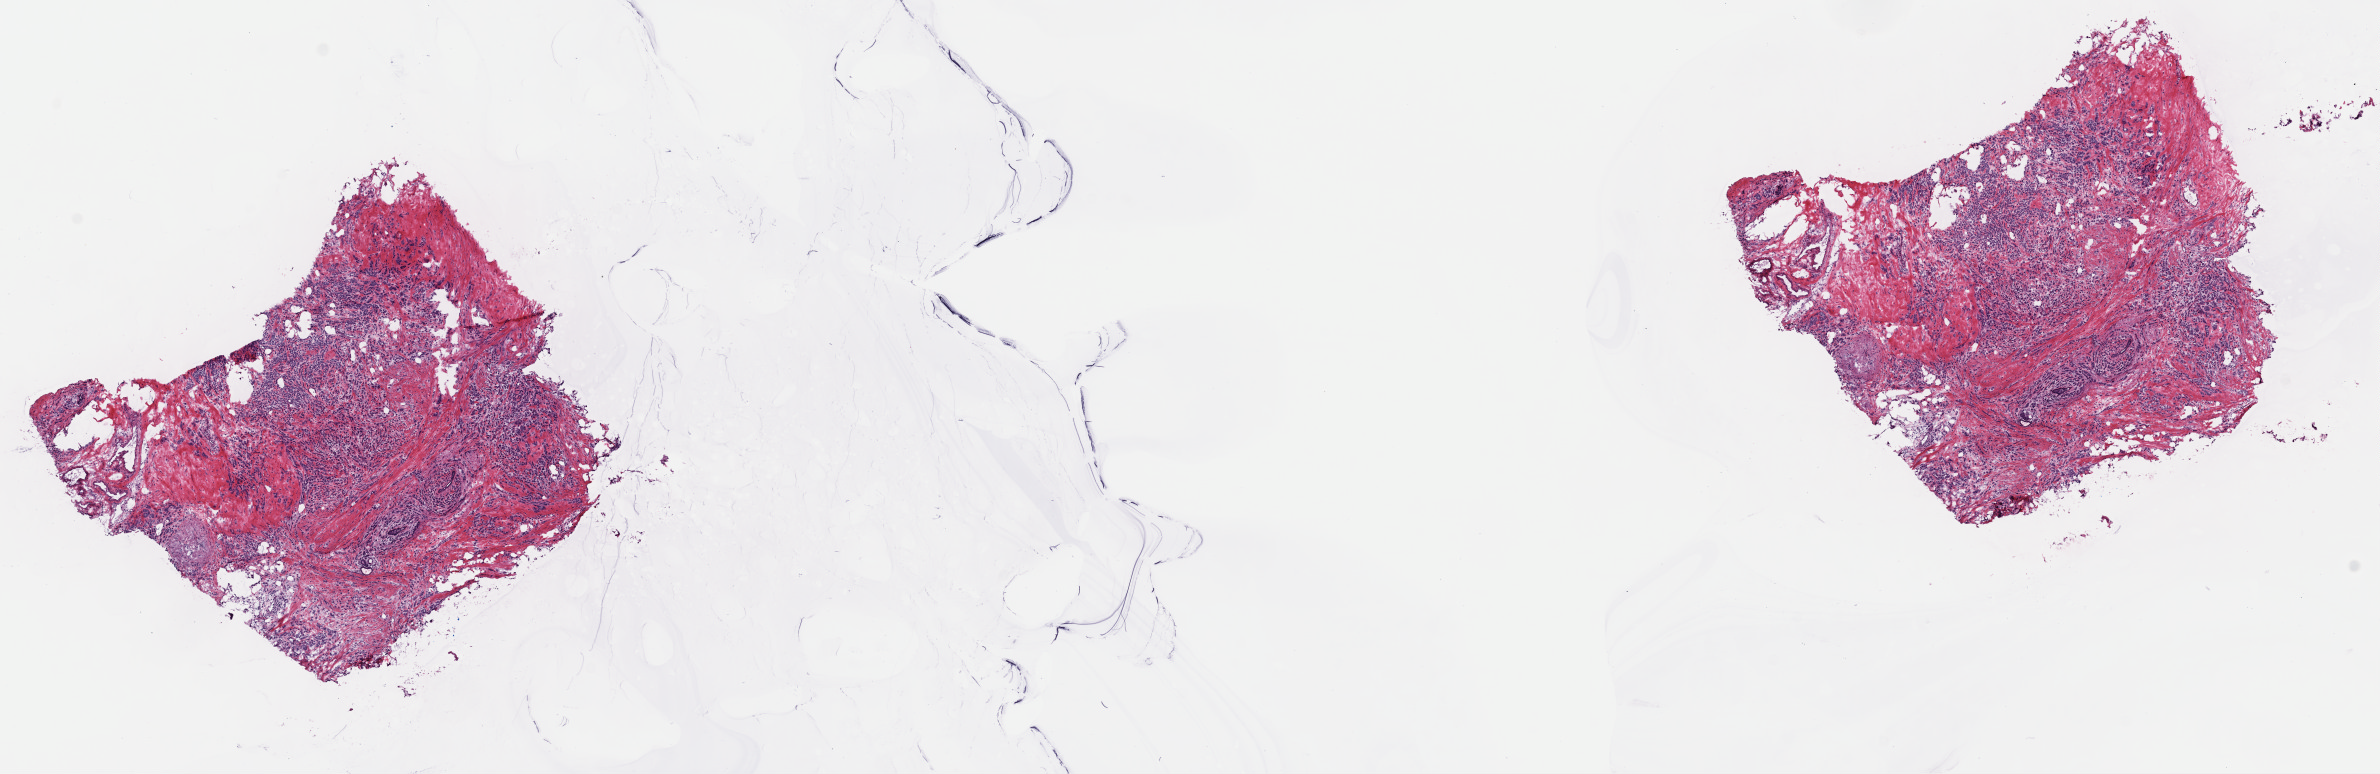
Whole-slide histology image, H&E-stained, whole scanned area (about 18.8 x 6.1 mm, slide scanned at 40x) shown as a low-resolution overview. Frozen section from the top of the tissue portion. Breast, primary tumour sample. Female patient; age at initial diagnosis 58 years. Pathologist review of this section (percent, as recorded): tumour cells 90%, tumour nuclei 85%, normal cells 5%, stromal cells 5%, necrosis 0%. Inflammatory infiltration, as recorded: lymphocyte infiltration 0%, monocyte infiltration 0%, neutrophil infiltration 0%.
AJCC pathologic stage: IIIA. Histologic diagnosis: Lobular carcinoma, NOS. Lymph nodes positive (case pathology): 4 of 10 examined. Laterality: right.